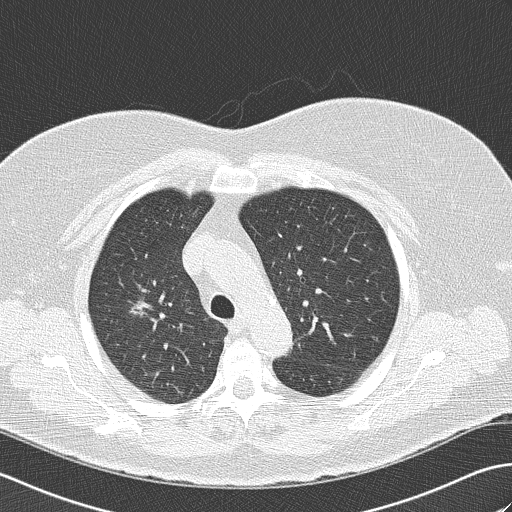
Chest CT (low-dose screening protocol), one axial image. Second screening round (one year after baseline). Lung window (W 1500 / L -600 HU). 2 mm slice thickness. Slice 114 of 148 in the series. 512 × 512 image matrix, field of view 350 × 350 mm. Female, age 74 years at enrolment. Former smoker at enrolment.
Lesion marked by an expert reader, bounding box [x1, y1, x2, y2] px = [104, 281, 171, 336]. The screening reader recorded 4 non-calcified nodules or masses ≥4 mm on this exam (right upper lobe, right middle lobe, right middle lobe, left lower lobe); which of them this box marks is not recorded. Official screen result: positive, other. Later outcome: lung cancer diagnosed 453 days after this screen (after the third annual screen) — bronchiolo-alveolar carcinoma, non-mucinous, right upper lobe, well differentiated (G1), stage IA (AJCC 6th edition), 14 mm at pathology.